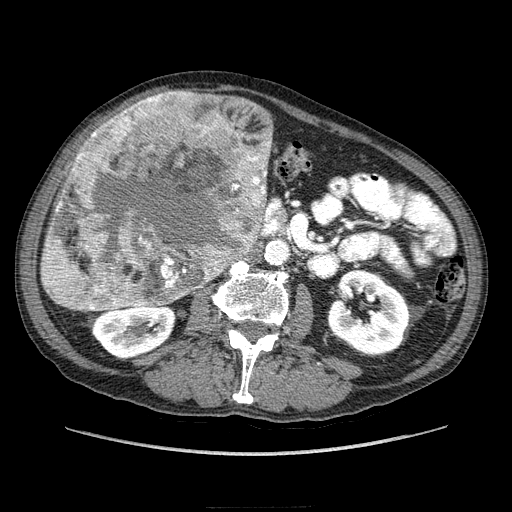
Contrast-enhanced abdominal CT (liver protocol), one axial slice; slice 83 of 218 in the series (ordered by position); reconstruction kernel STANDARD; 100 kVp; soft-tissue window (W 400 / L 40 HU); 2.5 mm slice thickness; 512 × 512 image matrix. From the clinical record (not read from this slice): diagnosis: hepatocellular carcinoma (patient treated with transarterial chemoembolisation; whether this scan precedes or follows treatment is not stated here); TNM stage (as recorded): Stage-IIIA; Child-Pugh class: A; tumour size: 20 cm.
Annotated regions visible in this slice (semi-automatic segmentation, software-assisted and operator-edited):
- liver parenchyma outside the tumour (the mass and vessels are separate outlines, so this box may not span the whole liver): box from (x=61, y=305) to (x=68, y=308) px
- mass: (x=40, y=89)–(x=274, y=313)